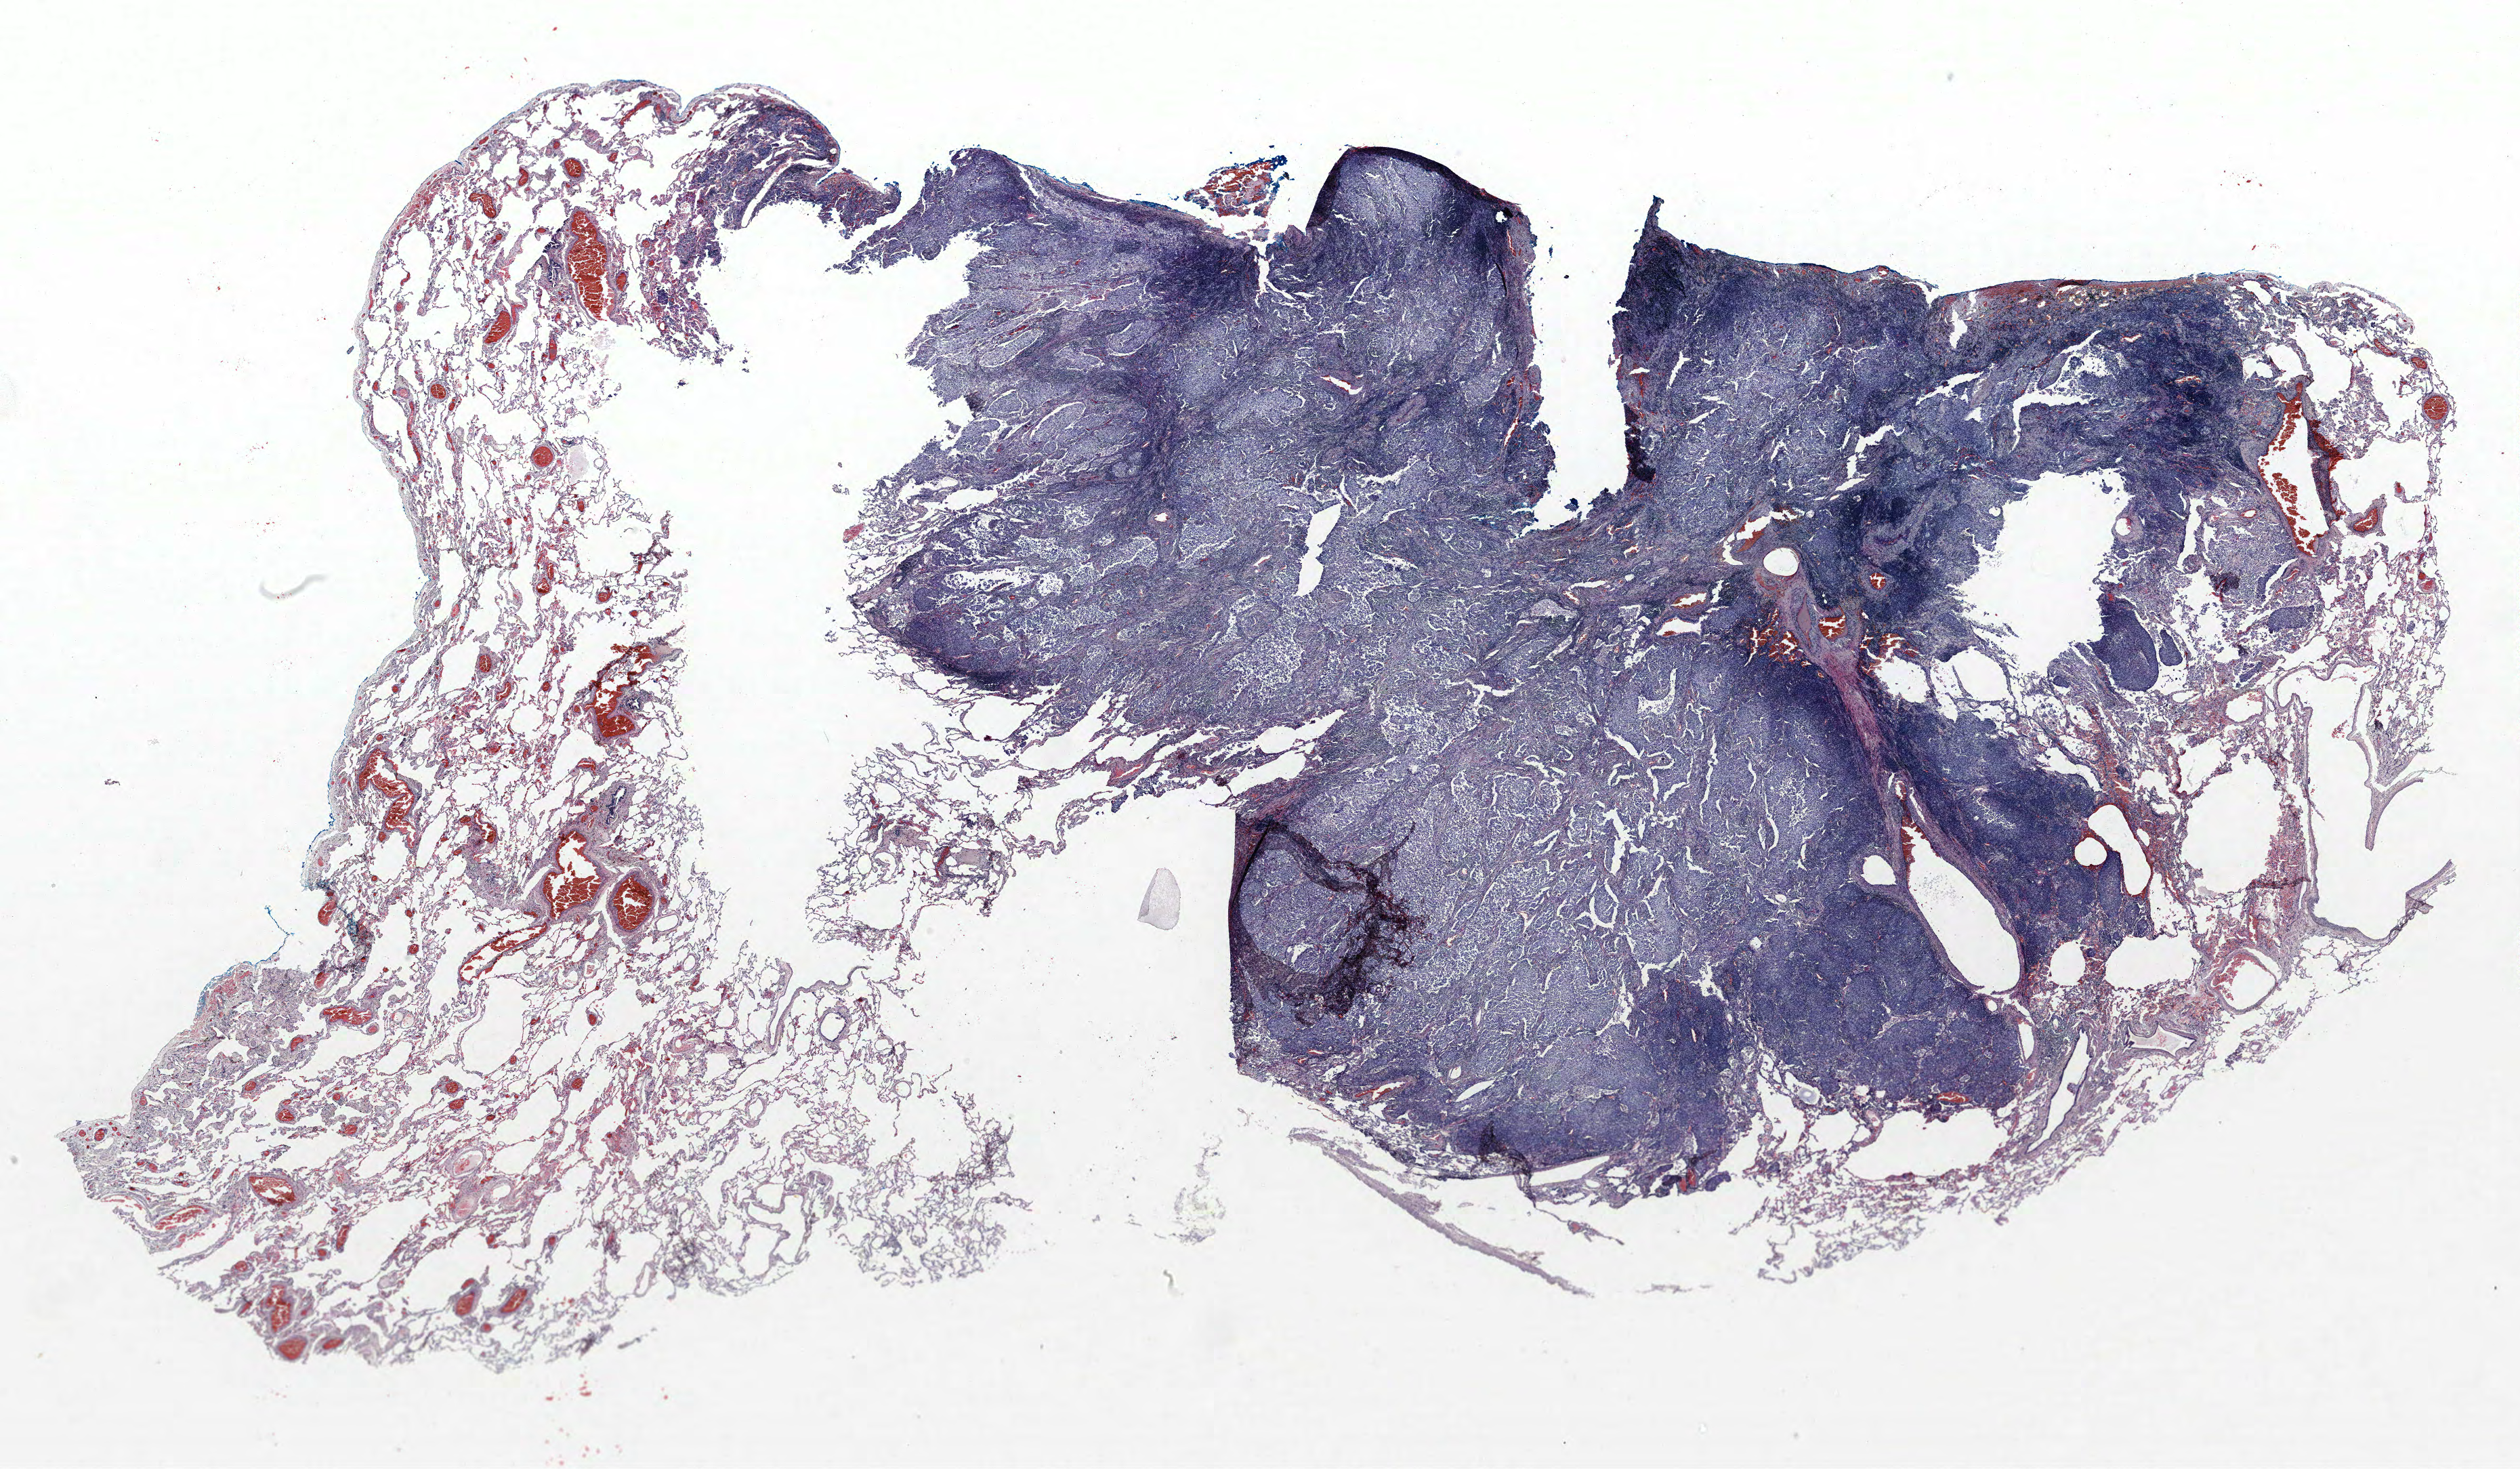
Hematoxylin and eosin (H&E) stained whole-slide image, a low-resolution overview of the entire scanned area, about 29.8 x 17.3 mm (acquisition: 40x scan); formalin-fixed paraffin-embedded (FFPE) section; lung. Male patient, aged 72 at enrolment. Current smoker at enrolment. Grade: moderately differentiated (G2).
Stage (AJCC 6th edition): IIA. Tumour size (pathology): 25 mm. Participant's lung-cancer diagnosis: Squamous cell carcinoma, NOS. Primary tumour location (clinical record): right upper lobe.